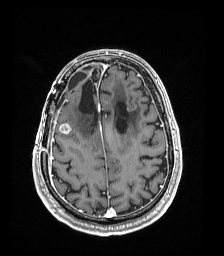
Brain MRI from a brain-tumour surgery series, one axial slice. Position 54 of 192 along the scan axis. T1-weighted post-contrast. 224 × 256 image matrix. Case-level facts recorded for this patient, not image findings: histopathology: Astrocytoma; WHO grade: 4; IDH mutation: yes; tumour location: Right Frontal.
Outlined on this slice (manually delineated by an expert):
- previous resection cavity: bounding box <78,69,98,123> (left, top, right, bottom; pixels)